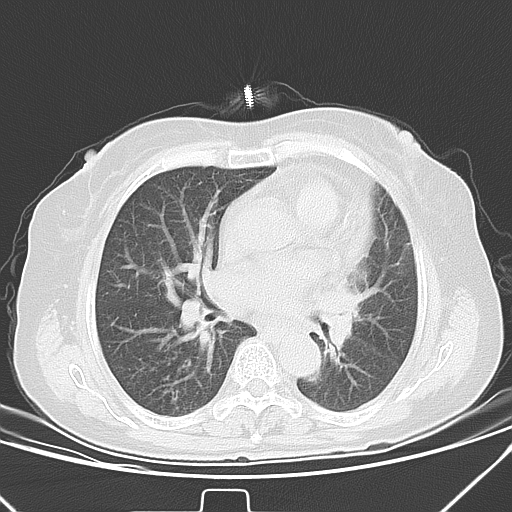
Chest CT, one axial slice; position 21 of 40 along the scan axis; lung window (W 1500 / L -600 HU); 512 × 512 image matrix. Female patient, age 59 years. Case-level facts recorded for this patient, not image findings: clinical TNM (as recorded): T3 N1 M0; histopathological grade: G3.
Annotated regions visible in this slice (bounding box drawn by a radiologist):
- lung tumour (recorded histology: small cell carcinoma): bounding box [x1, y1, x2, y2] px = [322, 287, 374, 370]